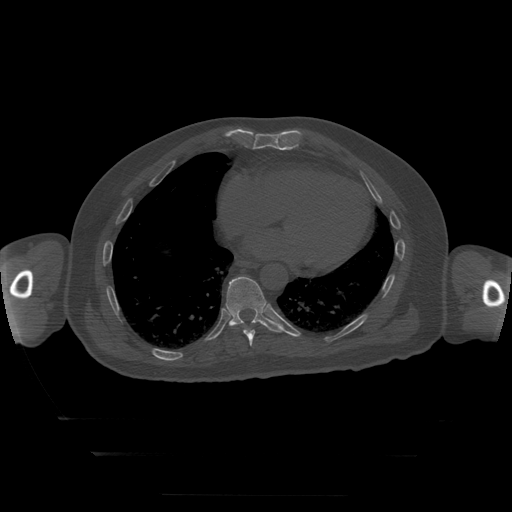
CT including the spine, one axial slice. Slice 132 of 397 in the series (ordered by position). Reconstruction kernel STANDARD. 120 kVp. Bone window (W 1800 / L 400 HU). 1.25 mm slice thickness. 512 × 512 image matrix, field of view 510 × 510 mm. Patient age 73 years. Case-level facts recorded for this patient, not image findings: primary cancer: prostate.
Structures marked on this image (semi-automatic segmentation, software-assisted and operator-edited):
- T10 vertebra: bounding box <226,277,285,333> (left, top, right, bottom; pixels)
- T9 vertebra: <244,329,256,346>